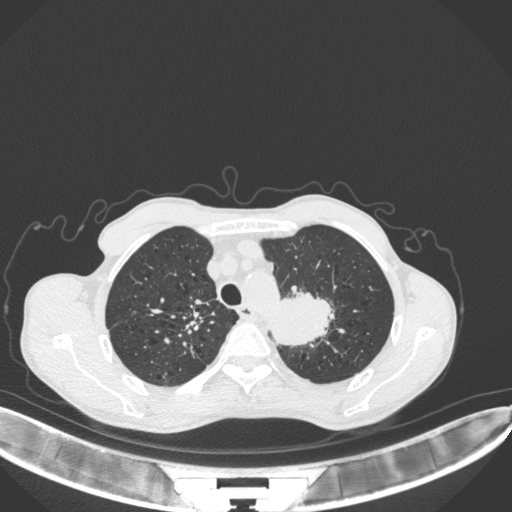
Chest CT, one axial slice; position 340 of 394 along the scan axis; reconstruction kernel B31f; 120 kVp; lung window (W 1500 / L -600 HU); 1 mm slice thickness; 512 × 512 image matrix, field of view 400 × 400 mm. Male patient, age 65 years. Case-level facts recorded for this patient, not image findings: clinical TNM (as recorded): T2b N0 M0.
Outlined on this slice (rectangle marked by the reading radiologist):
- lung tumour (recorded histology: adenocarcinoma): box from (x=265, y=289) to (x=337, y=346) px